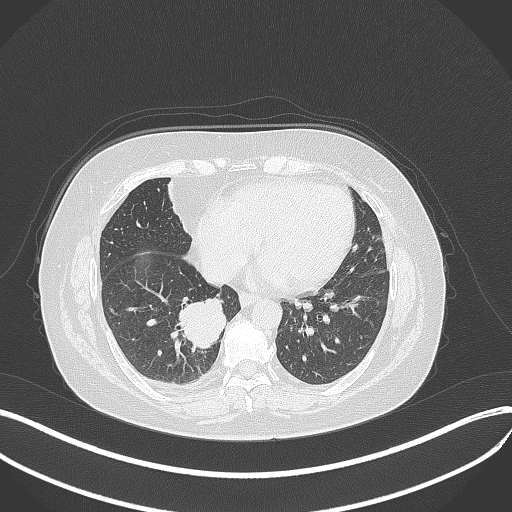
Chest CT, one axial slice; slice 128 of 381 in the series (ordered by position); reconstruction kernel B70f; 120 kVp; lung window (W 1500 / L -600 HU); 1 mm slice thickness; 512 × 512 image matrix, field of view 400 × 400 mm. Patient: female, 56 years. Case-level facts recorded for this patient, not image findings: clinical TNM (as recorded): T2b N1 M0; histopathological grade: G3.
Outlined on this slice (bounding box drawn by a radiologist):
- lung tumour (recorded histology: small cell carcinoma): bounding box (x1, y1, x2, y2) in pixels: (173, 293, 230, 351)